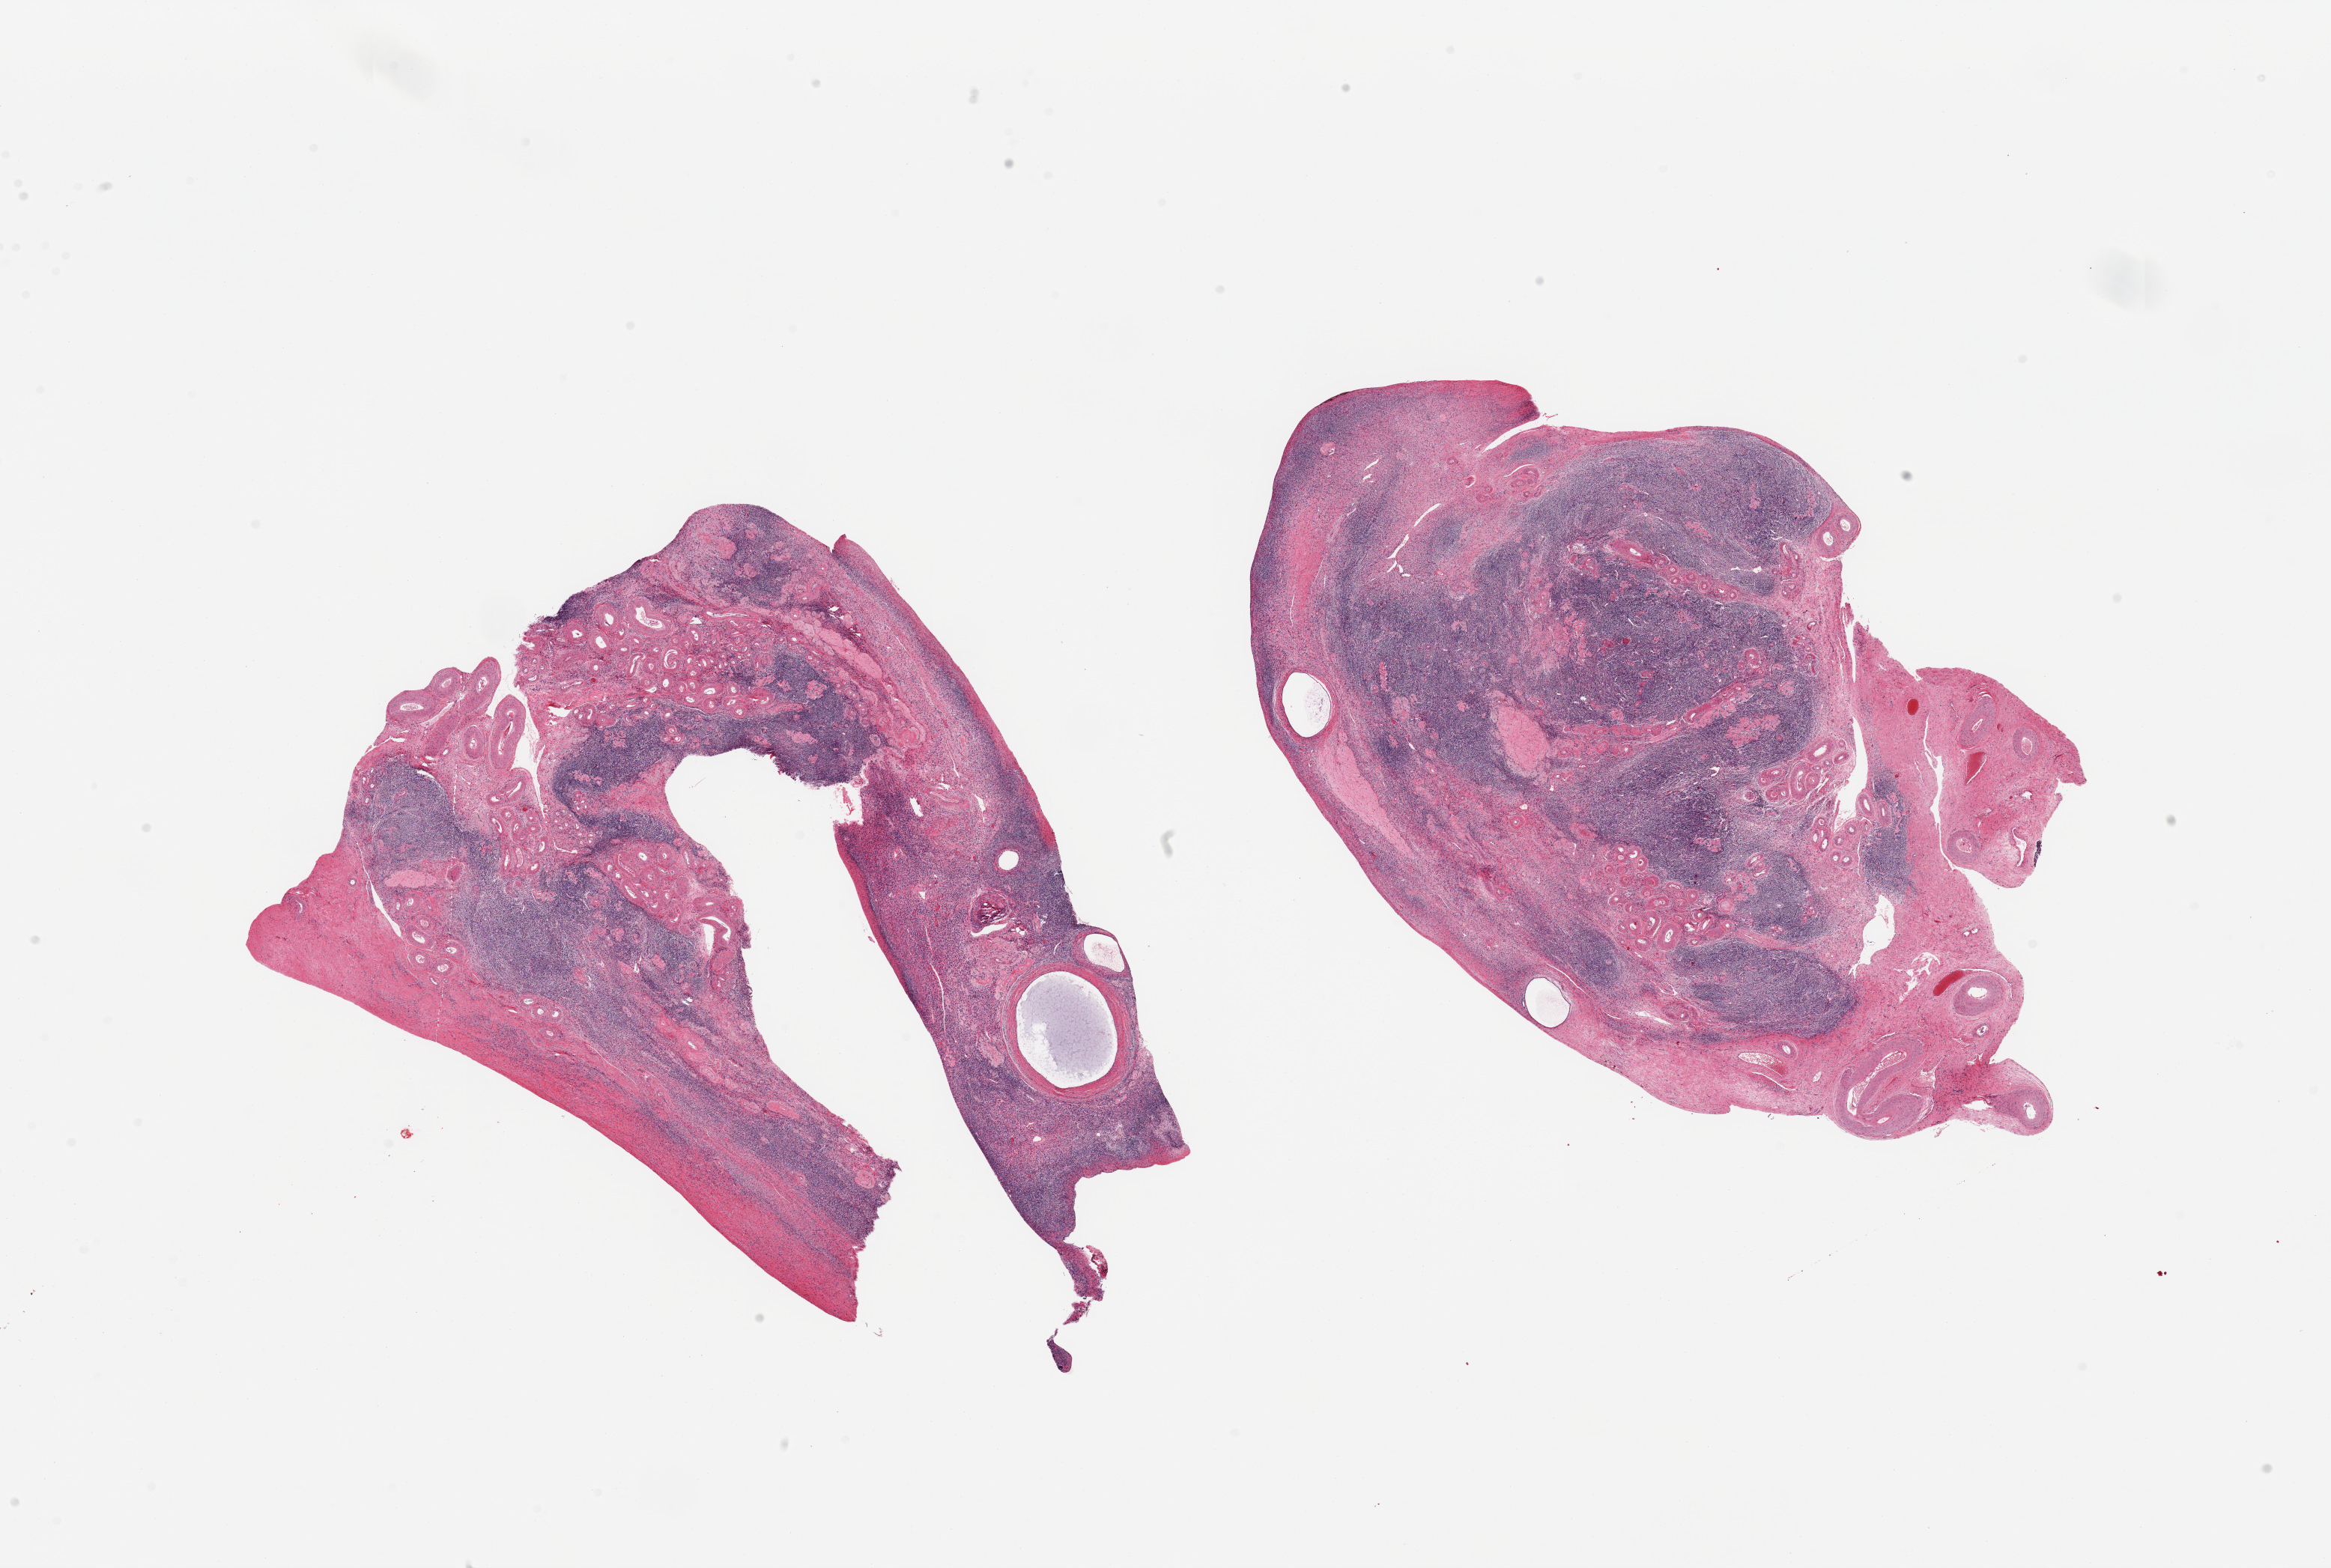
Whole-slide image, hematoxylin and eosin (H&E) stain, brightfield, a low-resolution overview of the entire scanned area, about 24.6 x 16.6 mm (slide scanned at 20x). PAXgene-fixed, paraffin-embedded tissue. Sampled site (target tissue): ovary. Donor tissue sample. Female donor.
* review note (as recorded): 2 pieces, post menopausal involution, banal inclusion cysts